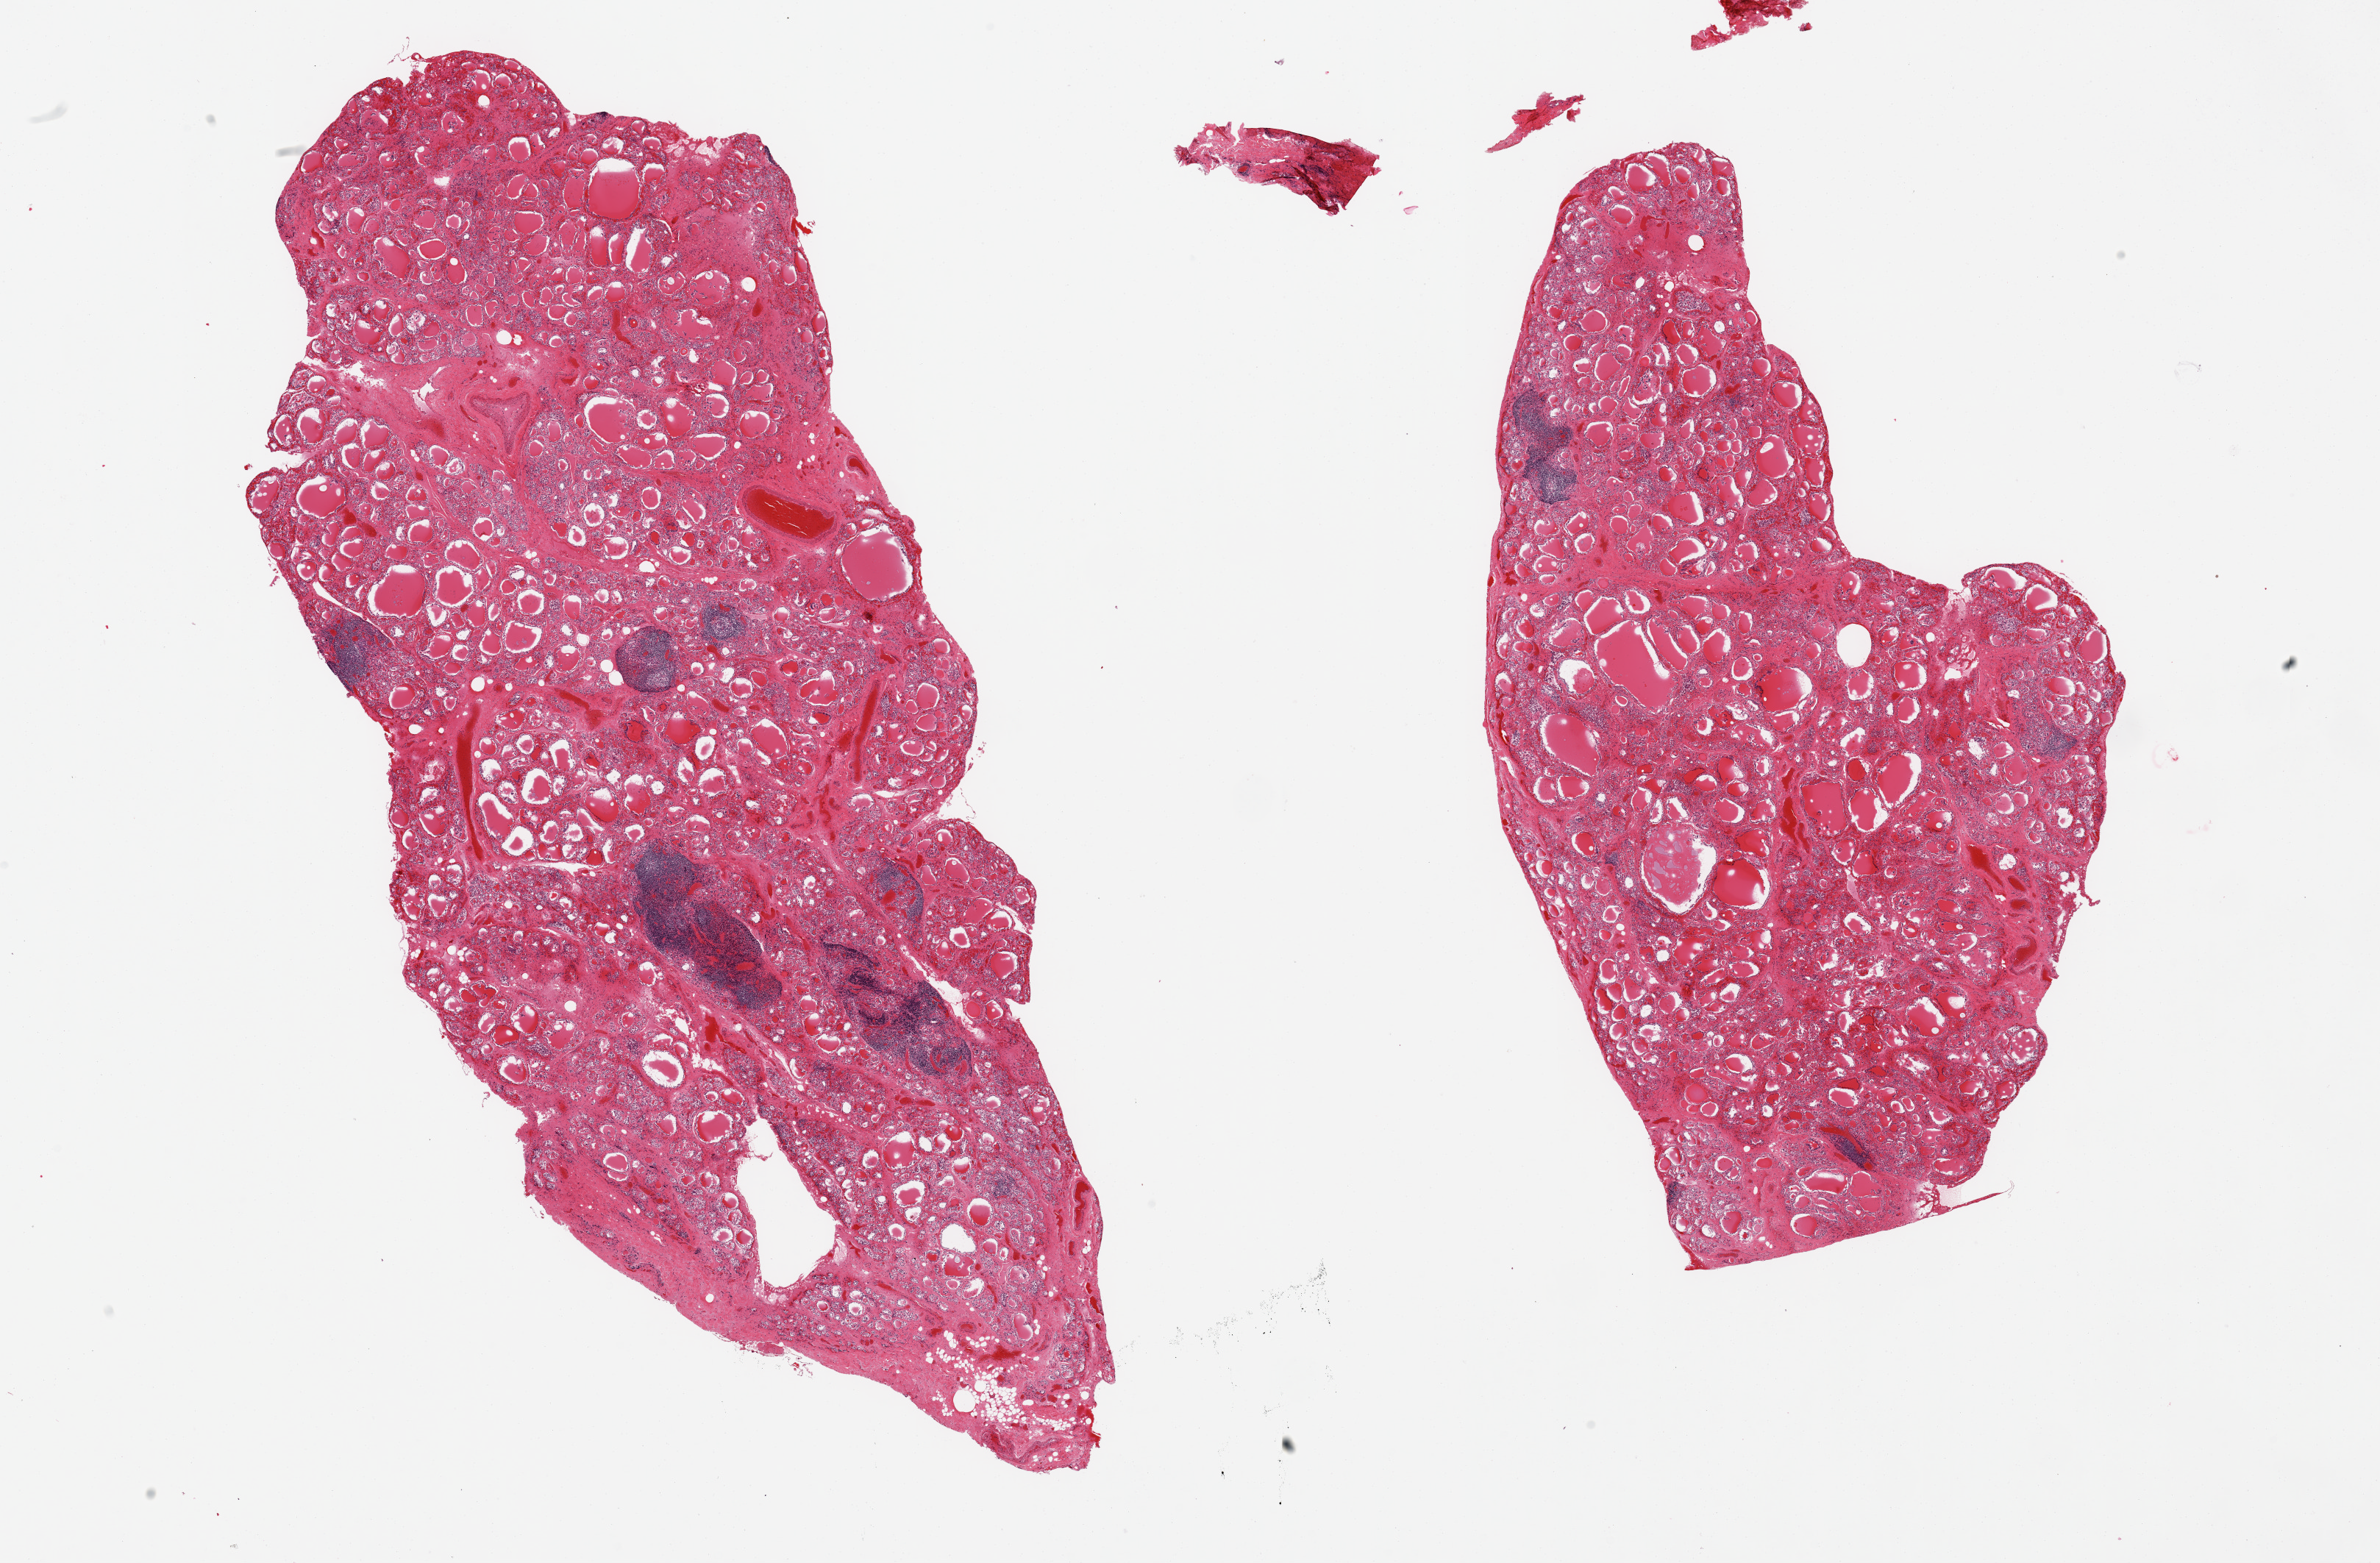
Whole-slide image, hematoxylin and eosin (H&E) stain — whole scanned area (about 25.6 x 16.8 mm) shown as a low-resolution overview. PAXgene-fixed, paraffin-embedded tissue. Sampled site (target tissue): thyroid. Tissue donor sample. Donor: male.
Reviewer comment on this tissue sample: 2 pieces; interstitial fibrosis and aggregates of lymphocytes consistent with Hashimoto thyroiditis; congestion.